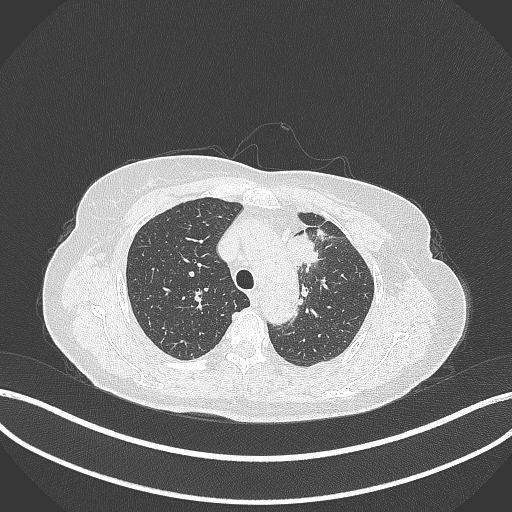
Chest CT, one axial slice; position 253 of 369 along the scan axis; reconstruction kernel B70f; lung window (W 1500 / L -600 HU); 1 mm slice thickness; 512 × 512 image matrix. Patient: female, 65 years. From the clinical record (not read from this slice): clinical TNM (as recorded): T2a N0 M0.
Annotated regions visible in this slice (rectangle marked by the reading radiologist):
- lung tumour (recorded histology: adenocarcinoma): bounding box (x1, y1, x2, y2) in pixels: (286, 230, 326, 269)